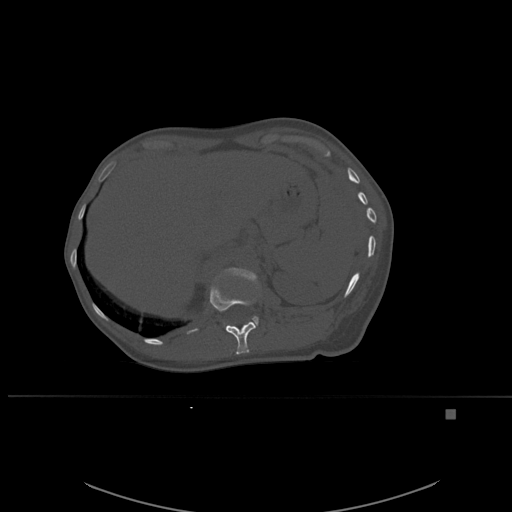
CT including the spine, one axial slice; slice 273 of 537 in the series (ordered by position); bone window (W 1800 / L 400 HU); 1.5 mm slice thickness; 512 × 512 image matrix. Patient: female, 45 years. From the clinical record (not read from this slice): primary cancer: lung.
Structures marked on this image (semi-automatic segmentation, software-assisted and operator-edited):
- L1 vertebra: box from (x=218, y=268) to (x=259, y=329) px
- T12 vertebra: (x=210, y=278)–(x=256, y=355)